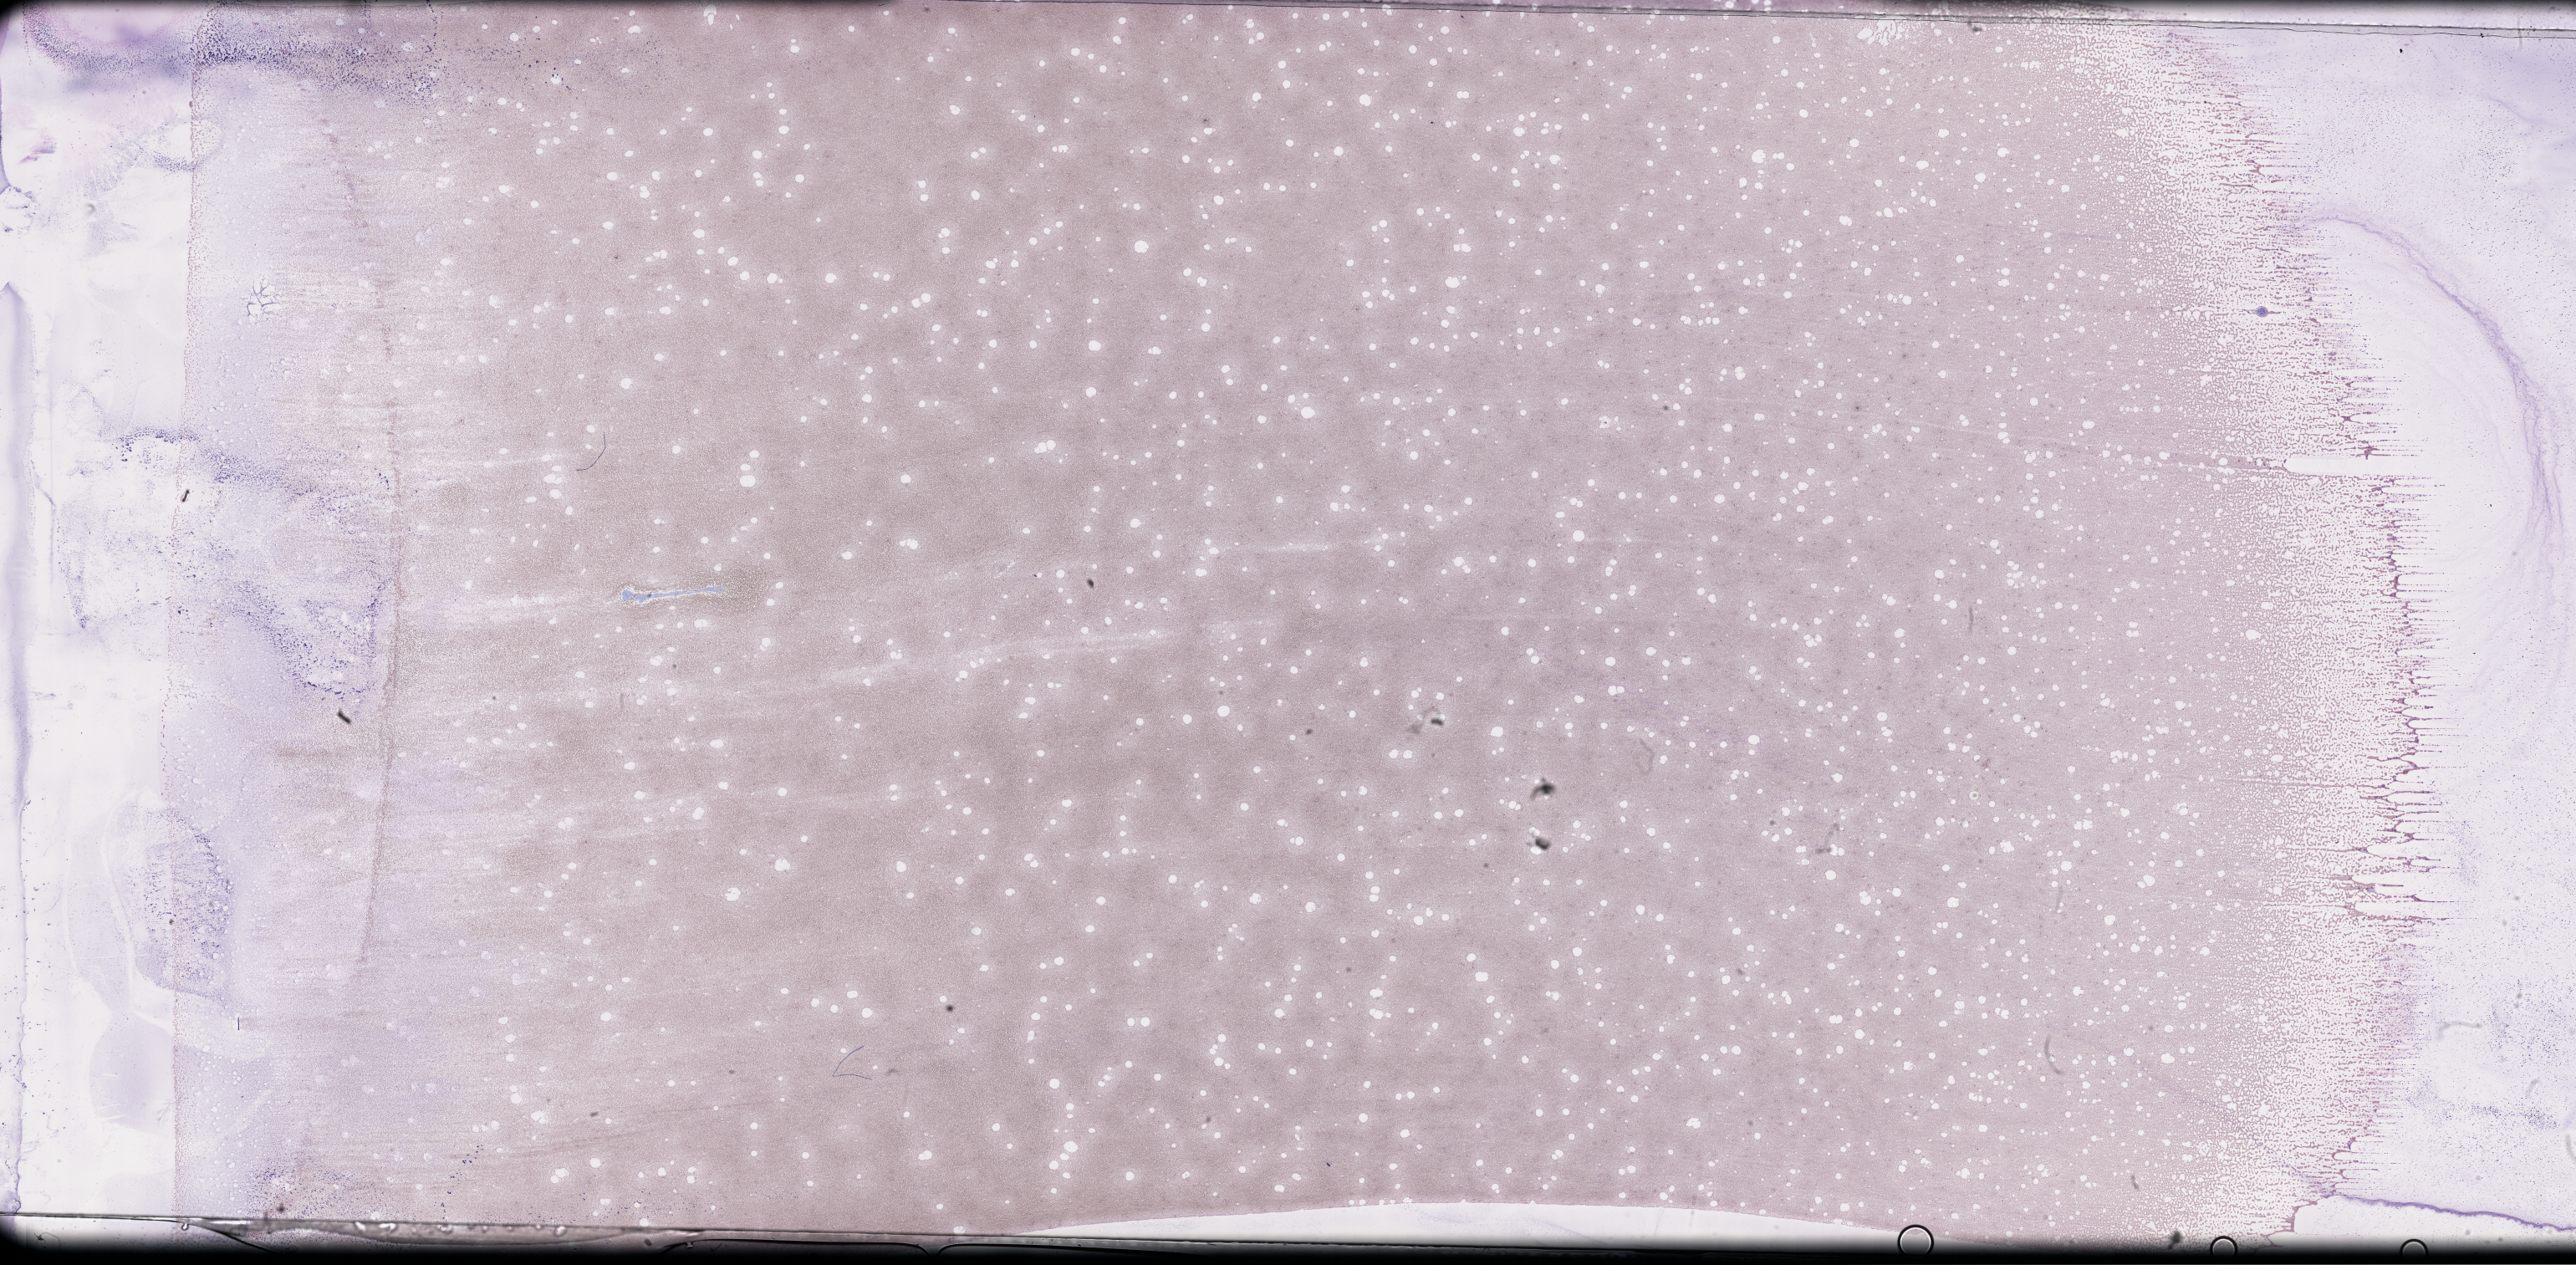
Whole-slide image of a whole blood smear, Wright–Giemsa stain, low-resolution overview of the scanned area, about 49.8 x 24.4 mm; EDTA-anticoagulated smear; collected at disease progression. Patient sex: female.
• patient diagnosis: Plasma Cell Myeloma